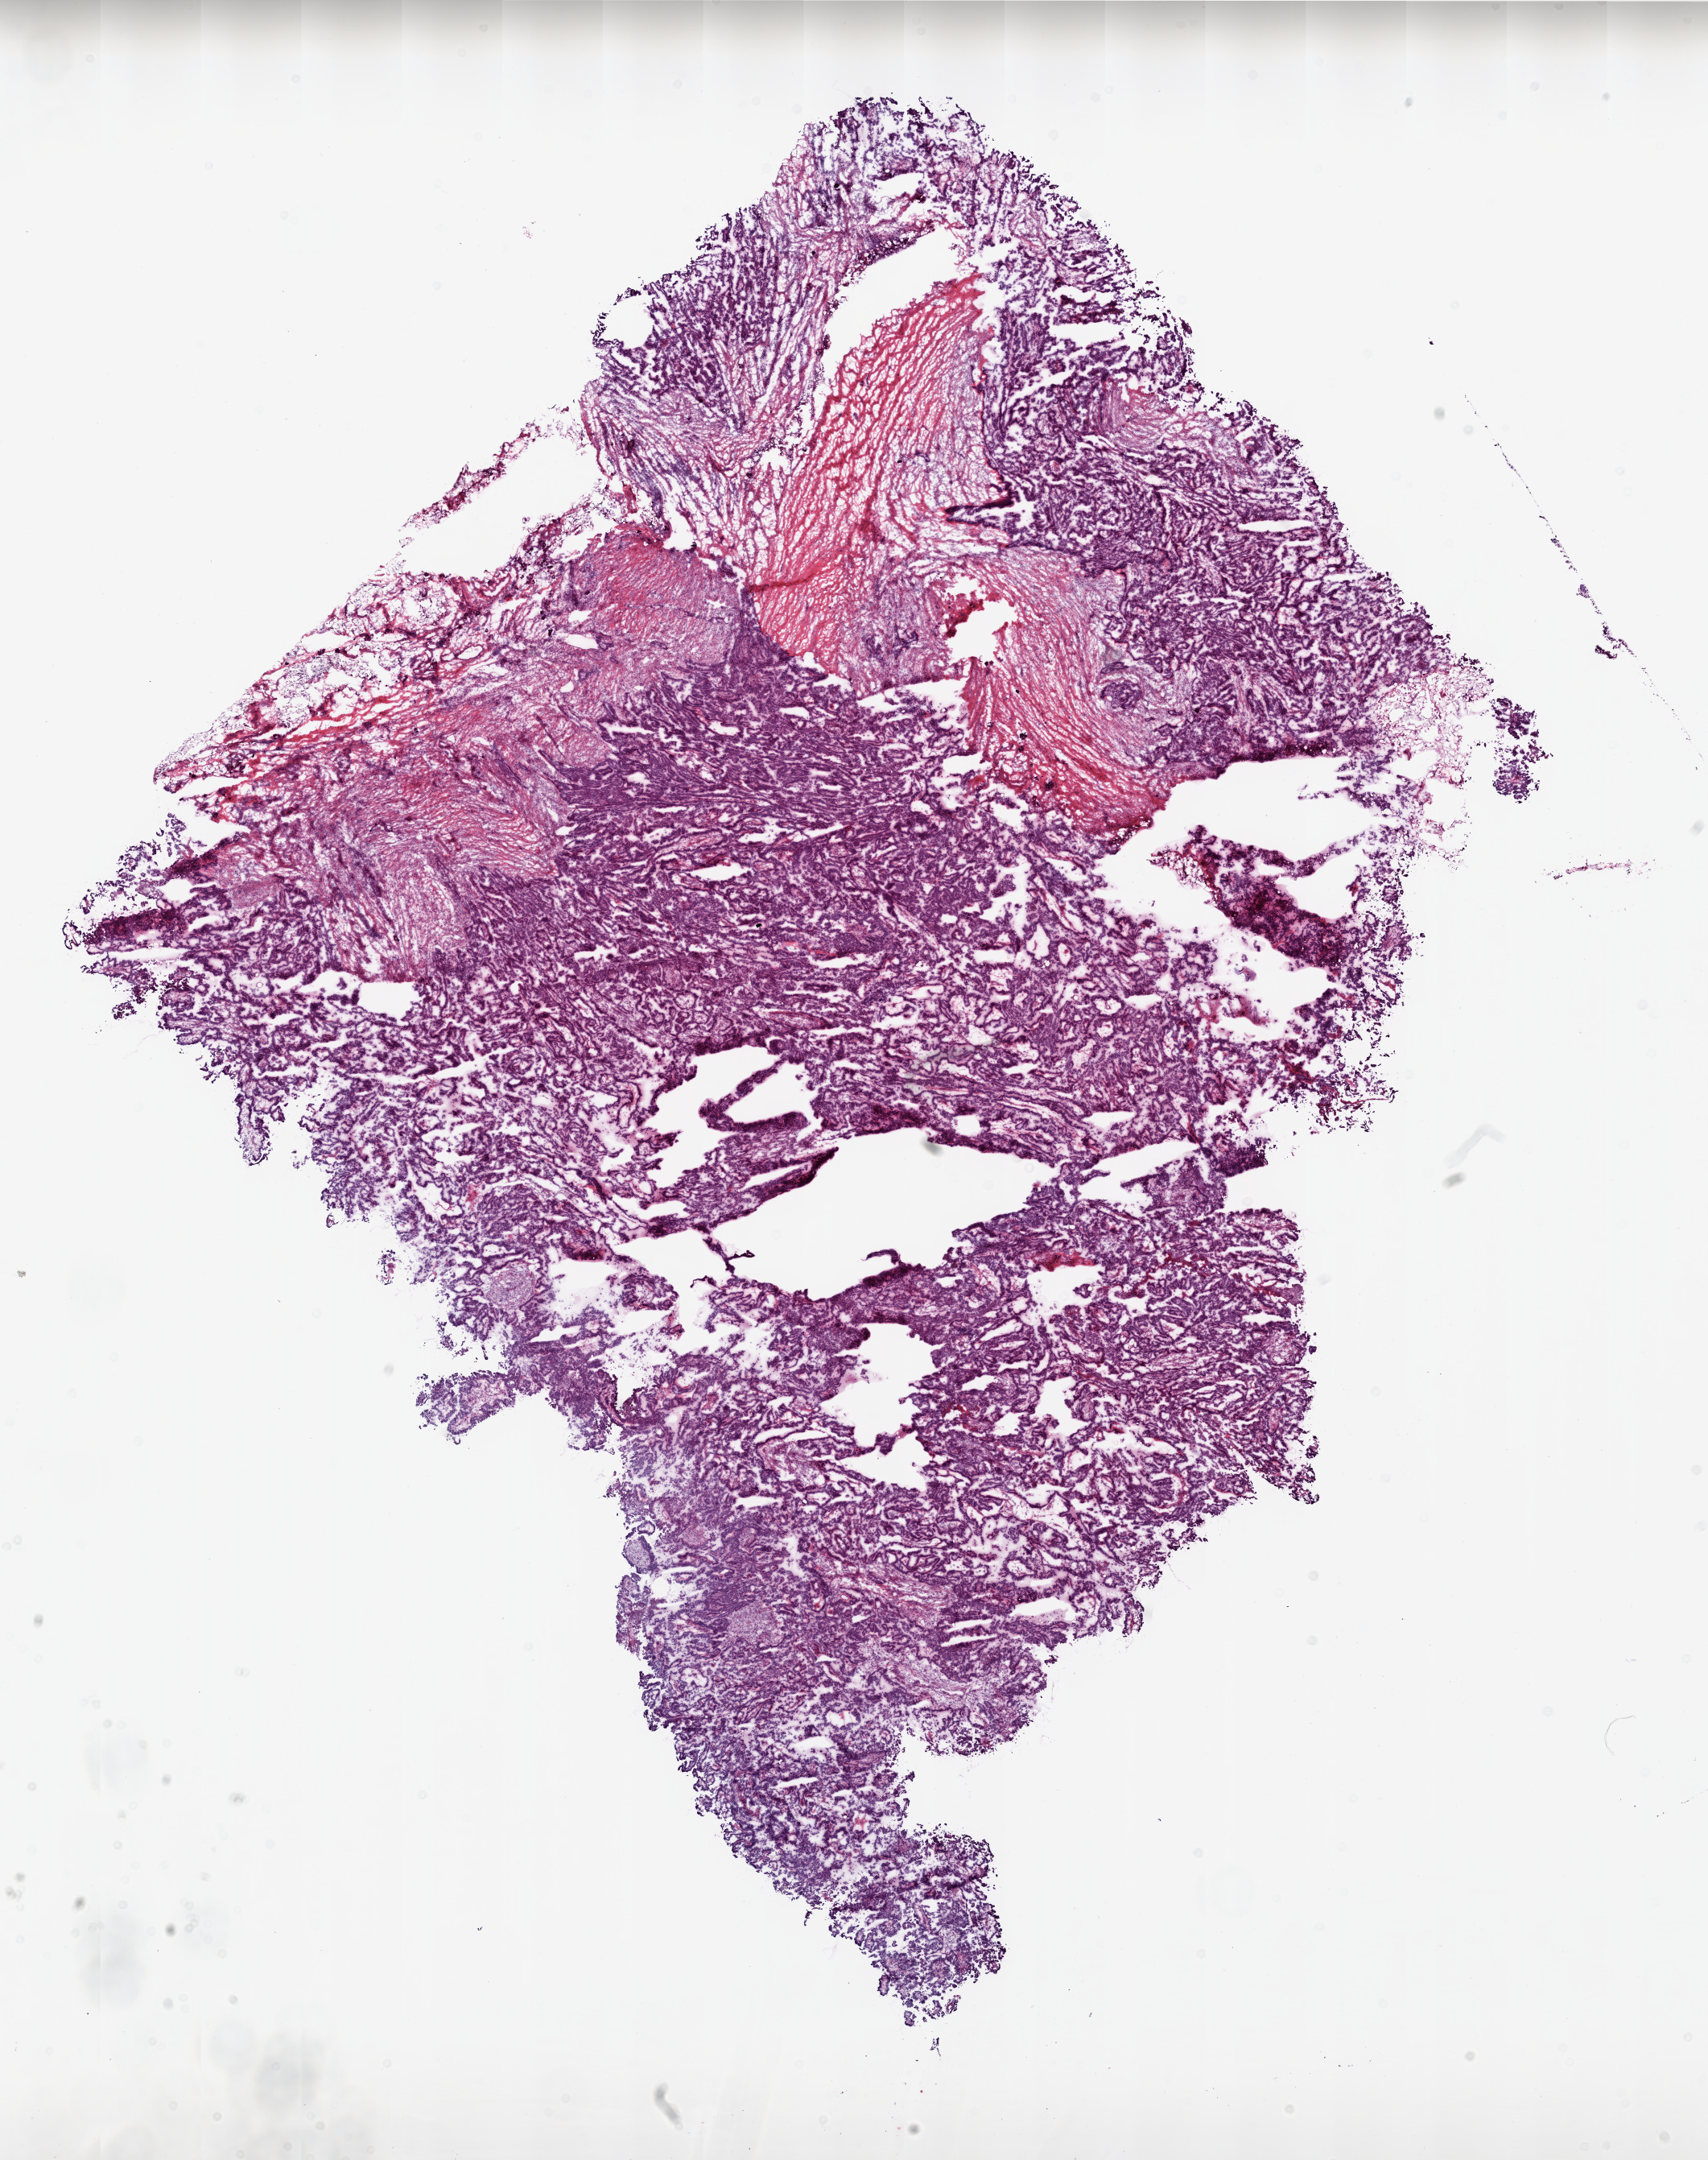
Whole-slide histology image, Hematoxylin and eosin (H&E) stained, shown as a low-resolution overview of the whole scanned area (about 17.0 x 21.5 mm, from a 20x scan), frozen section, primary tumour sample from the ovary. Female patient; age at initial diagnosis 60 years.
Pathologic diagnosis: Serous cystadenocarcinoma, NOS.